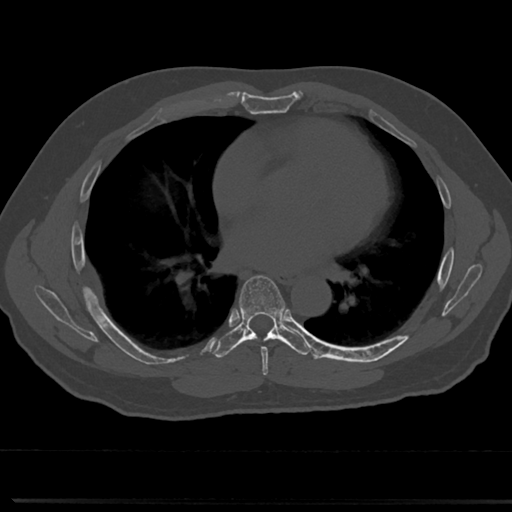
CT including the spine, one axial slice; slice 418 of 817 in the series (ordered by position); reconstruction kernel Br40s/3; 120 kVp; bone window (W 1800 / L 400 HU); 512 × 512 image matrix. Patient: male, 61 years. From the clinical record (not read from this slice): primary cancer: prostate.
Outlined on this slice (semi-automatically segmented with operator editing):
- T6 vertebra: bounding box <241,281,286,361> (left, top, right, bottom; pixels)
- T7 vertebra: <239,275,286,335>